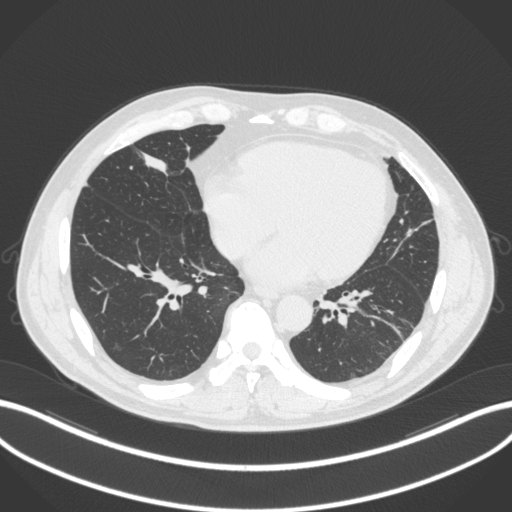
Chest CT, one axial slice. 120 kVp. Lung window (W 1500 / L -600 HU). 512 × 512 image matrix. Patient: male, 59 years. From the clinical record (not read from this slice): clinical TNM (as recorded): T2a N1 M0.
Annotated regions visible in this slice (rectangle marked by the reading radiologist):
- lung tumour (recorded histology: adenocarcinoma): box from (x=137, y=145) to (x=183, y=181) px